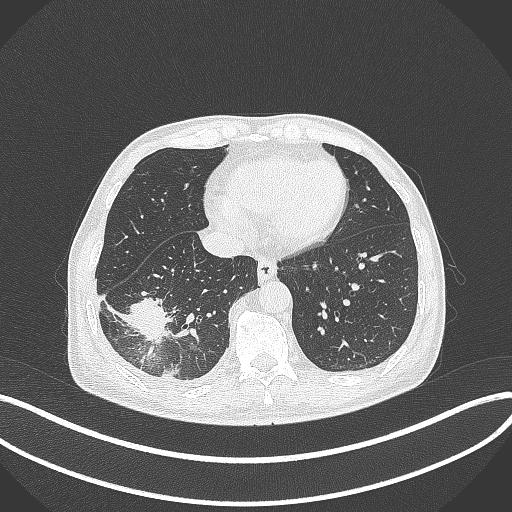
Chest CT, one axial slice. Slice 110 of 388 in the series (ordered by position). Reconstruction kernel B70f. 120 kVp. Lung window (W 1500 / L -600 HU). 1 mm slice thickness. 512 × 512 image matrix, field of view 400 × 400 mm. Male patient, age 64 years. From the clinical record (not read from this slice): clinical TNM (as recorded): T3 N0 M0; histopathological grade: G2-3.
Outlined on this slice (rectangle marked by the reading radiologist):
- lung tumour (recorded histology: adenocarcinoma): bounding box (x1, y1, x2, y2) in pixels: (121, 291, 176, 344)